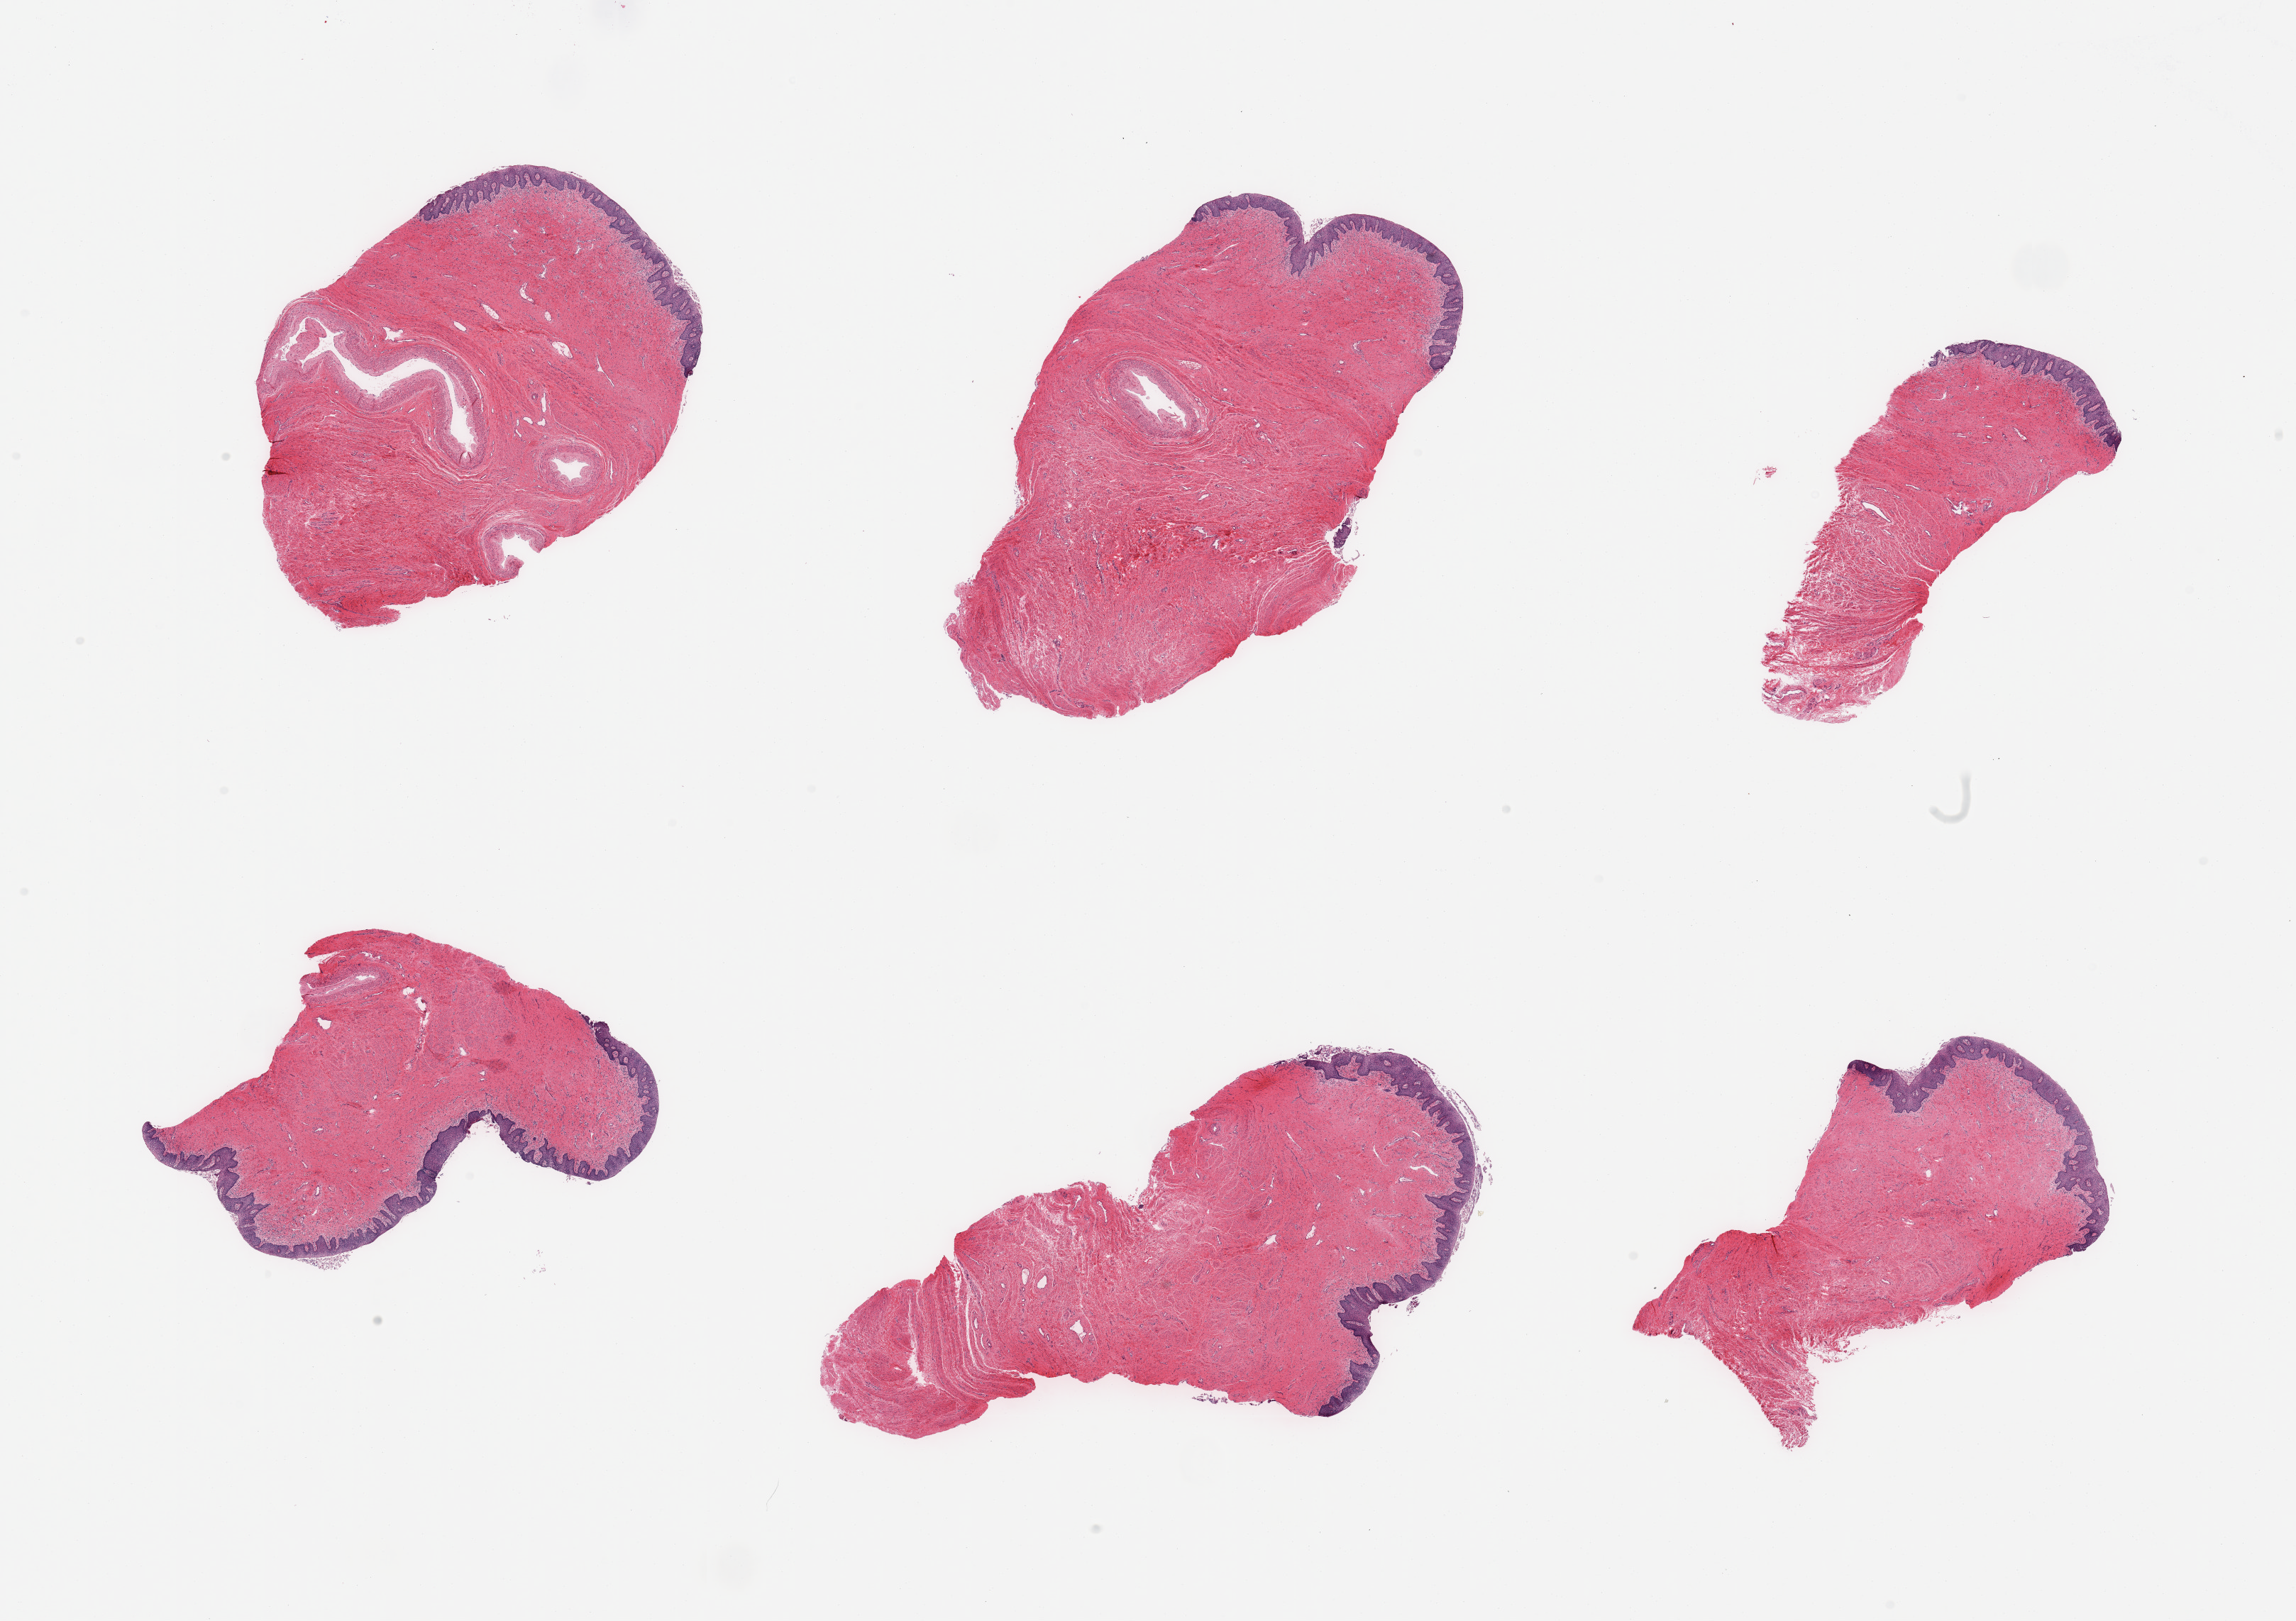
Whole-slide image, haematoxylin and eosin stain — a low-resolution overview of the entire scanned area, about 25.6 x 18.1 mm, PAXgene-fixed, paraffin-embedded tissue, section of vagina (target tissue), tissue donor sample.
Review note (as recorded): 6 pieces; epithelium partially sloughed, ~0.23mm.